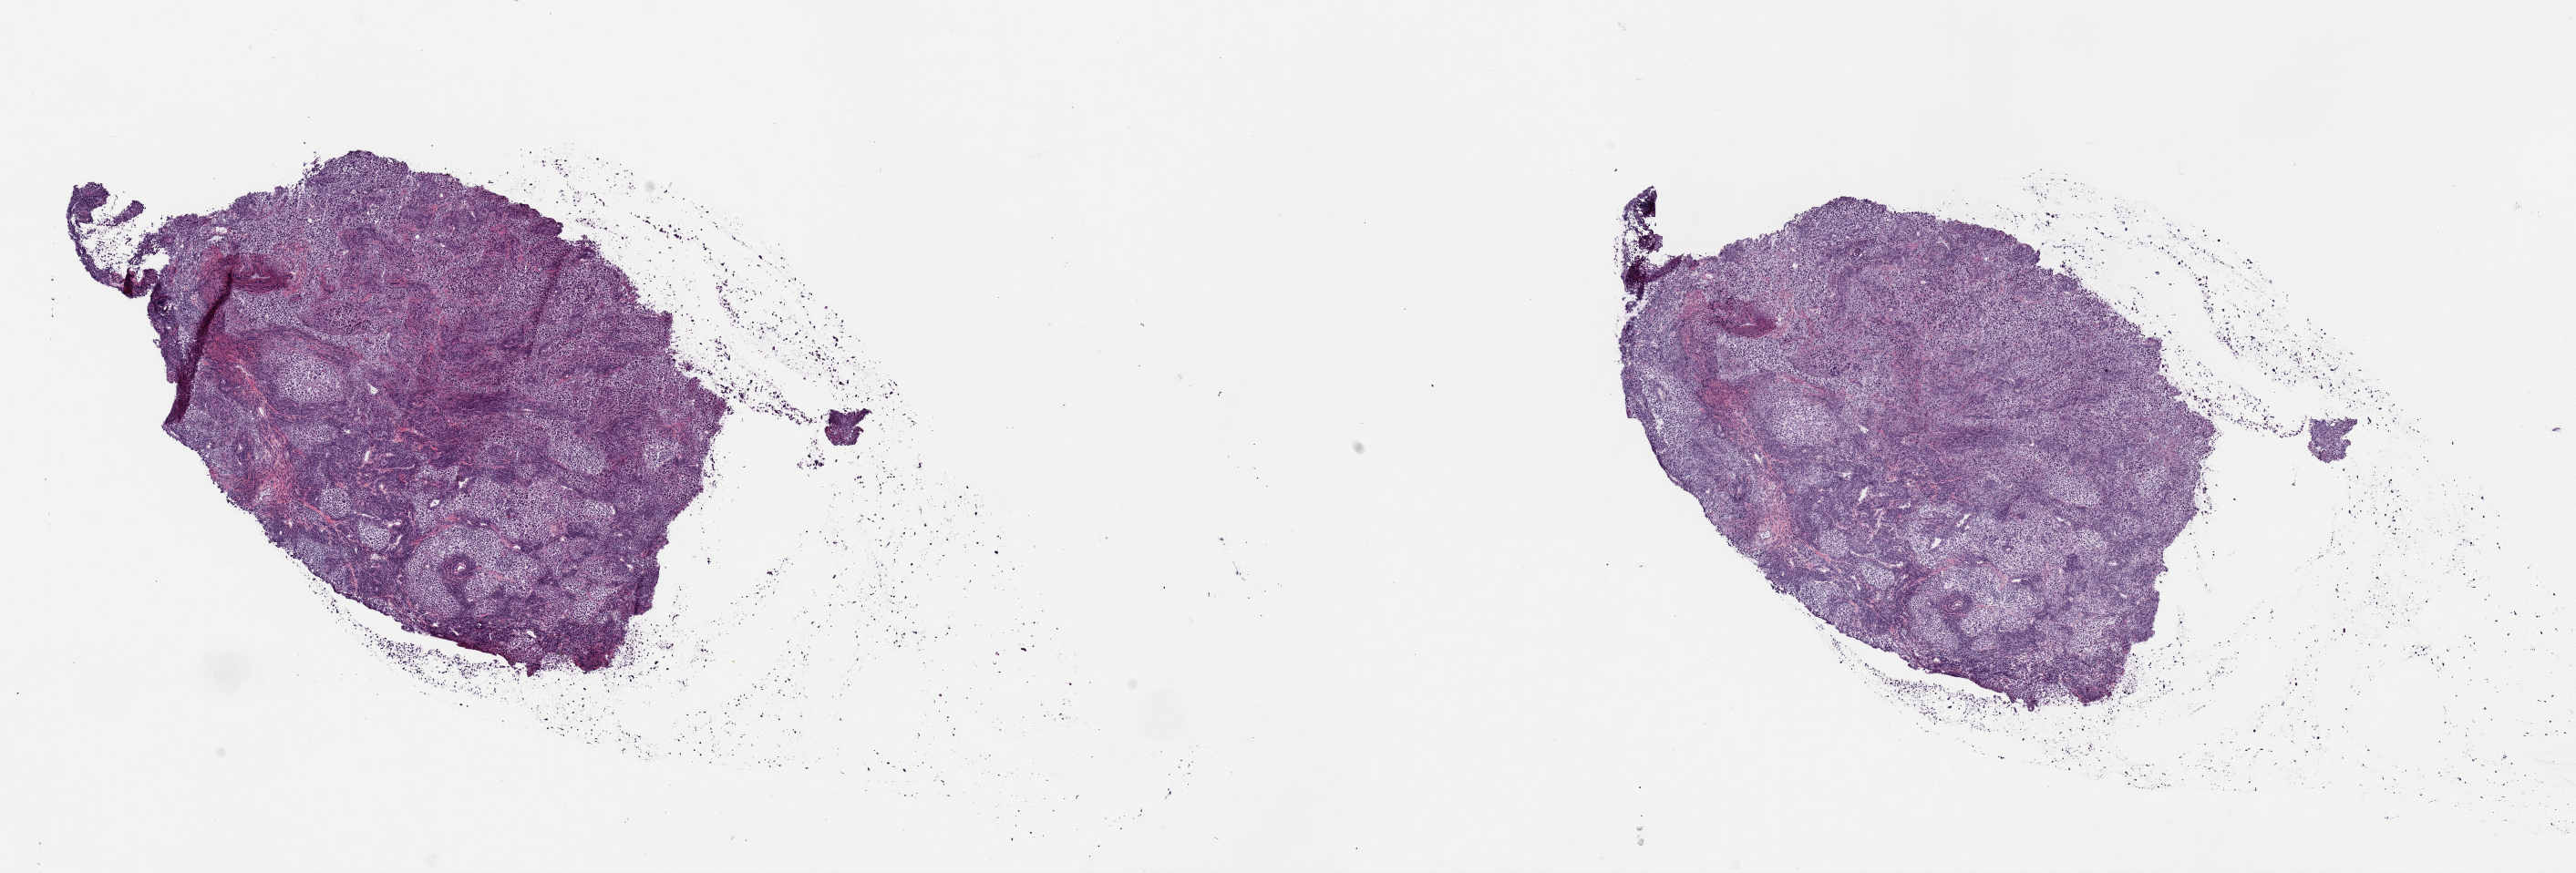
Digitized Hematoxylin and eosin (H&E) stained tissue section (whole slide) — a low-resolution overview of the entire scanned area, about 22.3 x 7.6 mm (slide scanned at 40x). Frozen section from the top of the tissue portion. Metastatic tumour sample, sampled site: lymph nodes of axilla or arm. Patient: female, age at initial diagnosis 74 years. Composition of this section per pathologist review: tumour cells 100%, tumour nuclei 65%, normal cells 0%, stromal cells 0%, necrosis 0%. Infiltration values recorded for this section: lymphocyte infiltration 15%, monocyte infiltration 0%, neutrophil infiltration 0%.
- this section: metastatic tumour tissue
- patient diagnosis: Malignant melanoma, NOS